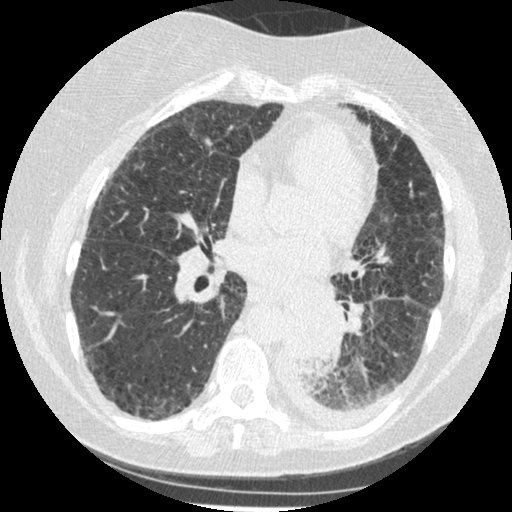
Low-dose screening chest CT, one axial slice. Position 110 of 341 along the scan axis. Reconstruction kernel STANDARD. 120 kVp. Lung window (W 1500 / L -600 HU). 1.25 mm slice thickness. 512 × 512 image matrix, field of view 310 × 310 mm.
Annotated regions visible in this slice (outlined manually by an expert reader):
- lesion 1 (tumor, lower lobe of left lung): bounding box (x1, y1, x2, y2) in pixels: (285, 302, 339, 365)